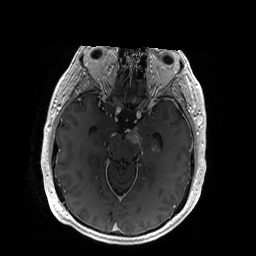
Brain MRI from a brain-tumour surgery series, one axial slice; position 116 of 192 along the scan axis; T1-weighted post-contrast; 1 mm slice thickness; 256 × 256 image matrix, field of view 256 × 256 mm. Case-level facts recorded for this patient, not image findings: histopathology: Glioblastoma; WHO grade: 4; IDH mutation: no.
Outlined on this slice (expert manual segmentation):
- tumour: bounding box [x1, y1, x2, y2] px = [126, 128, 159, 154]